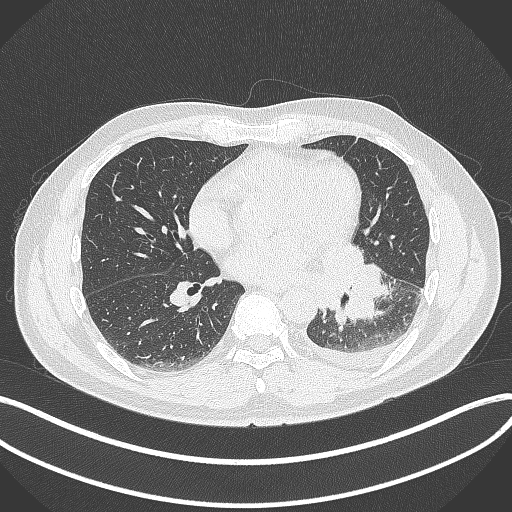
Chest CT, one axial slice. Slice 159 of 342 in the series (ordered by position). Lung window (W 1500 / L -600 HU). 1 mm slice thickness. 512 × 512 image matrix, field of view 400 × 400 mm. Patient: male, 58 years. Case-level facts recorded for this patient, not image findings: clinical TNM (as recorded): T3 N1 M1b; histopathological grade: G3.
Structures marked on this image (bounding box drawn by a radiologist):
- lung tumour (recorded histology: small cell carcinoma): bounding box <319,238,387,328> (left, top, right, bottom; pixels)